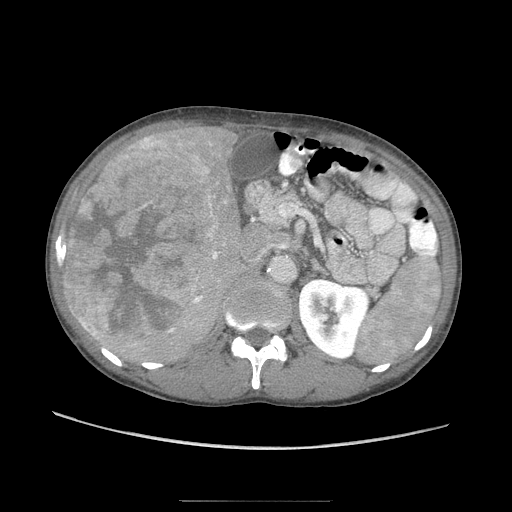
Contrast-enhanced abdominal CT (liver protocol), one axial slice. Slice 41 of 103 in the series (ordered by position). Reconstruction kernel STANDARD. Soft-tissue window (W 400 / L 40 HU). 2.5 mm slice thickness. 512 × 512 image matrix, field of view 380 × 380 mm. Case-level facts recorded for this patient, not image findings: diagnosis: hepatocellular carcinoma (patient treated with transarterial chemoembolisation; whether this scan precedes or follows treatment is not stated here); TNM stage (as recorded): Stage-IIIA; Child-Pugh class: A; tumour differentiation: moderately differentiated; tumour size: 16 cm.
Outlined on this slice (semi-automatically segmented with operator editing):
- liver parenchyma outside the tumour (the mass and vessels are separate outlines, so this box may not span the whole liver): bounding box [x1, y1, x2, y2] px = [62, 124, 254, 362]
- mass: [63, 133, 220, 347]
- liver vessels: [83, 144, 221, 330]